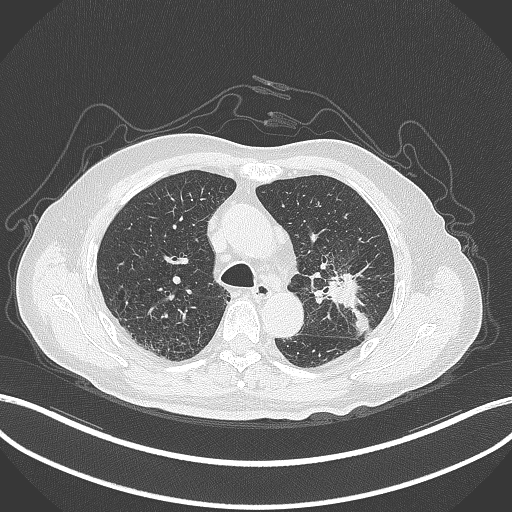
Chest CT, one axial slice; slice 195 of 331 in the series (ordered by position); 120 kVp; lung window (W 1500 / L -600 HU); 512 × 512 image matrix, field of view 400 × 400 mm. Patient: male, 79 years. From the clinical record (not read from this slice): clinical TNM (as recorded): T2a N1 M1.
Outlined on this slice (rectangle marked by the reading radiologist):
- lung tumour (recorded histology: adenocarcinoma): bounding box (x1, y1, x2, y2) in pixels: (328, 269, 374, 339)